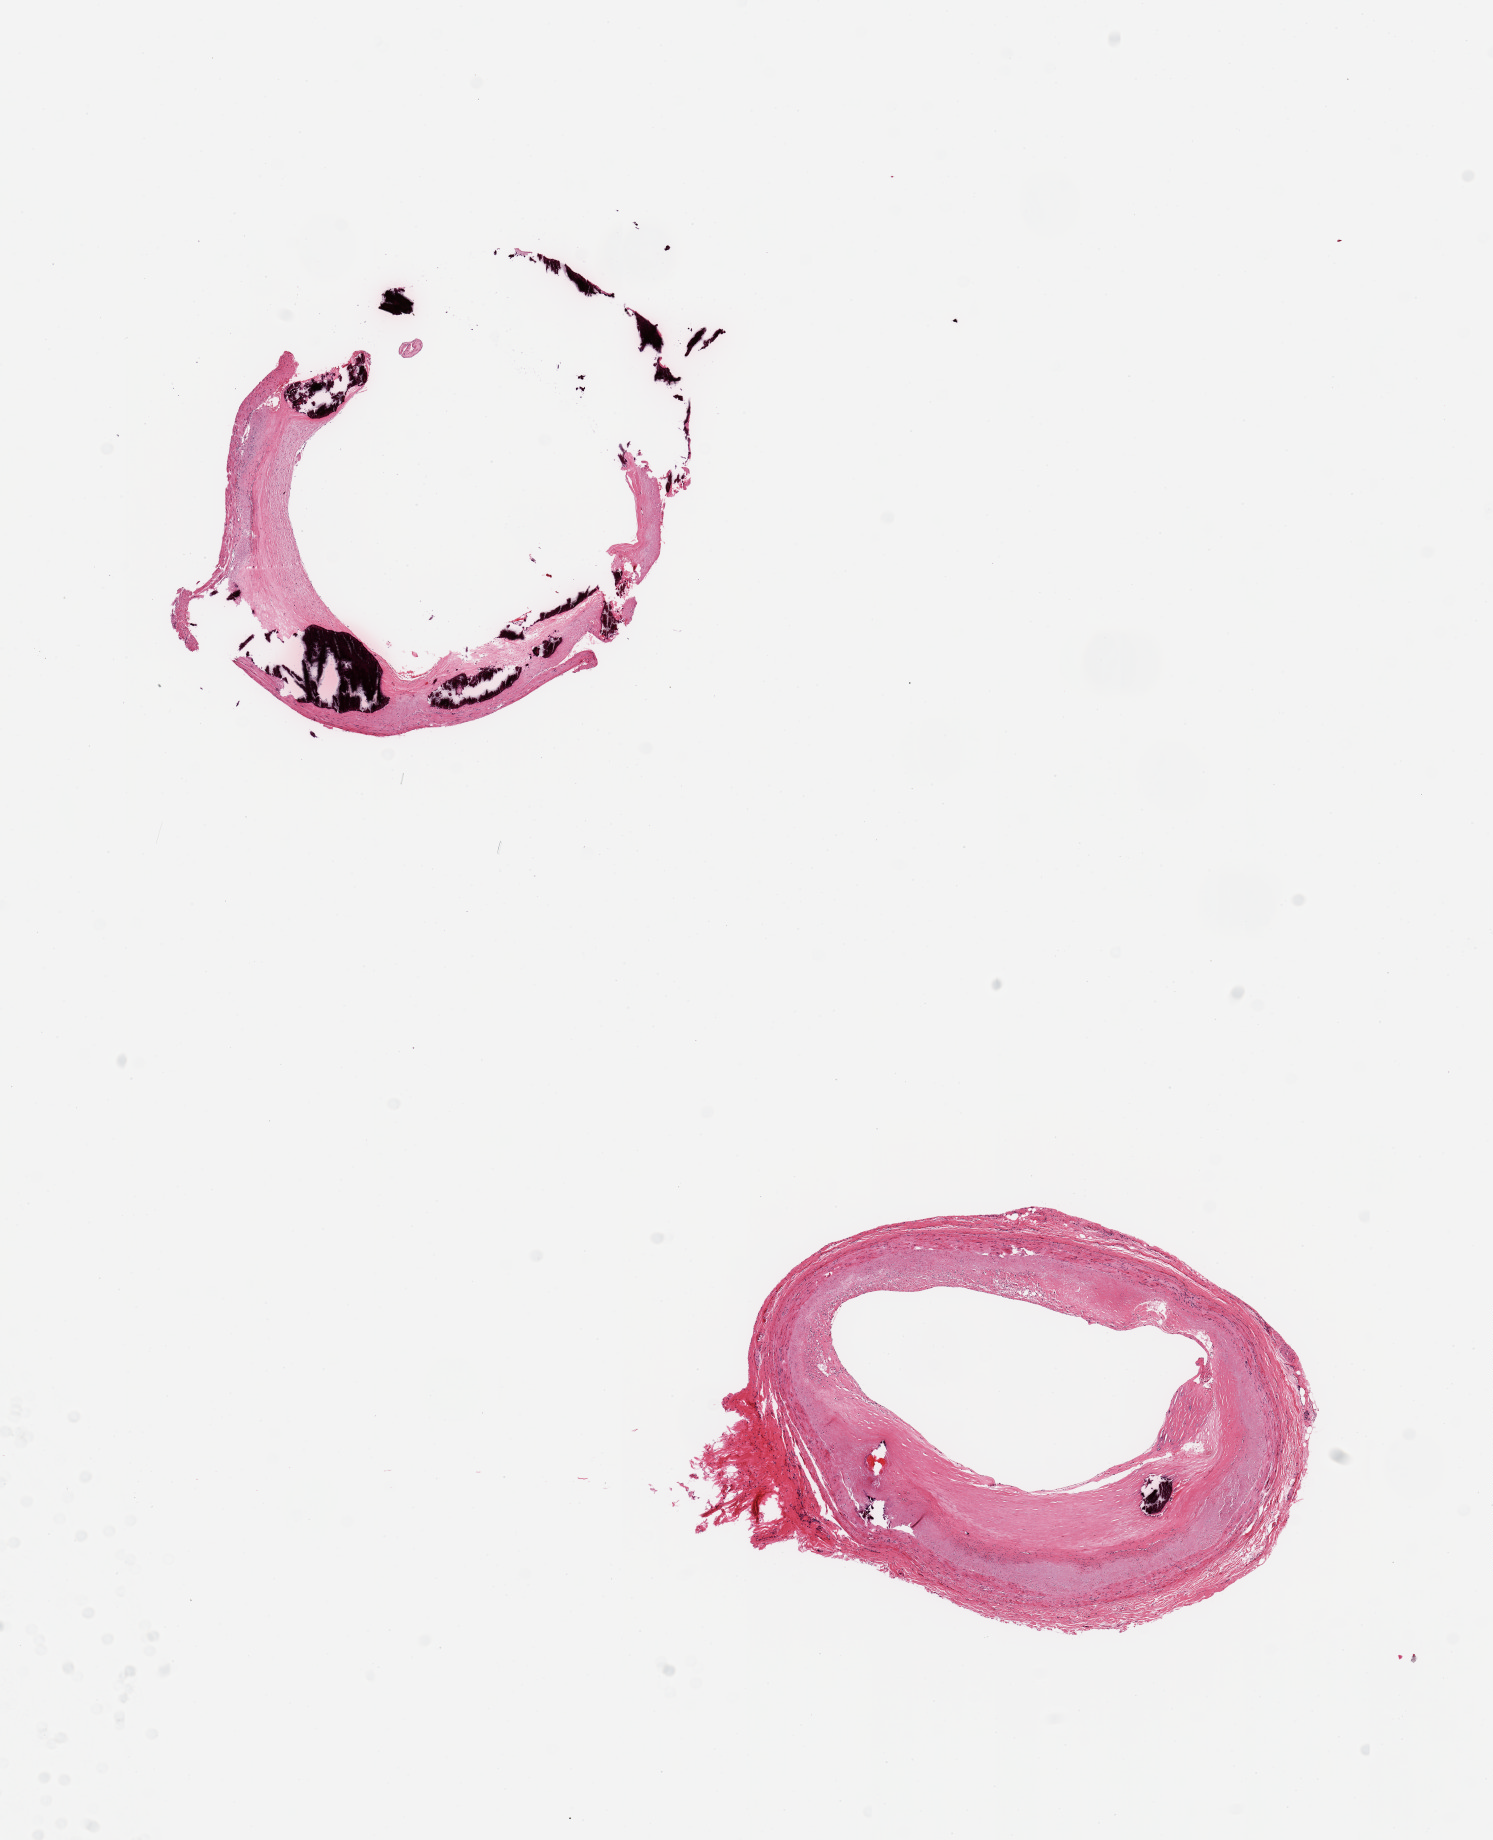
Whole-slide image, haematoxylin and eosin stain, shown as a low-resolution overview of the whole scanned area (about 11.8 x 14.6 mm, acquisition: 20x scan); PAXgene-fixed paraffin-embedded (PFPE) section; sampled site (target tissue): coronary artery; donor tissue sample. Donor sex: female.
Pathologist's review note for this sample: 2 pieces; 1 with concentric fibrosis, focal calcification and patent lumen; other is largely calcified and fibrotic with mural fragmentation.